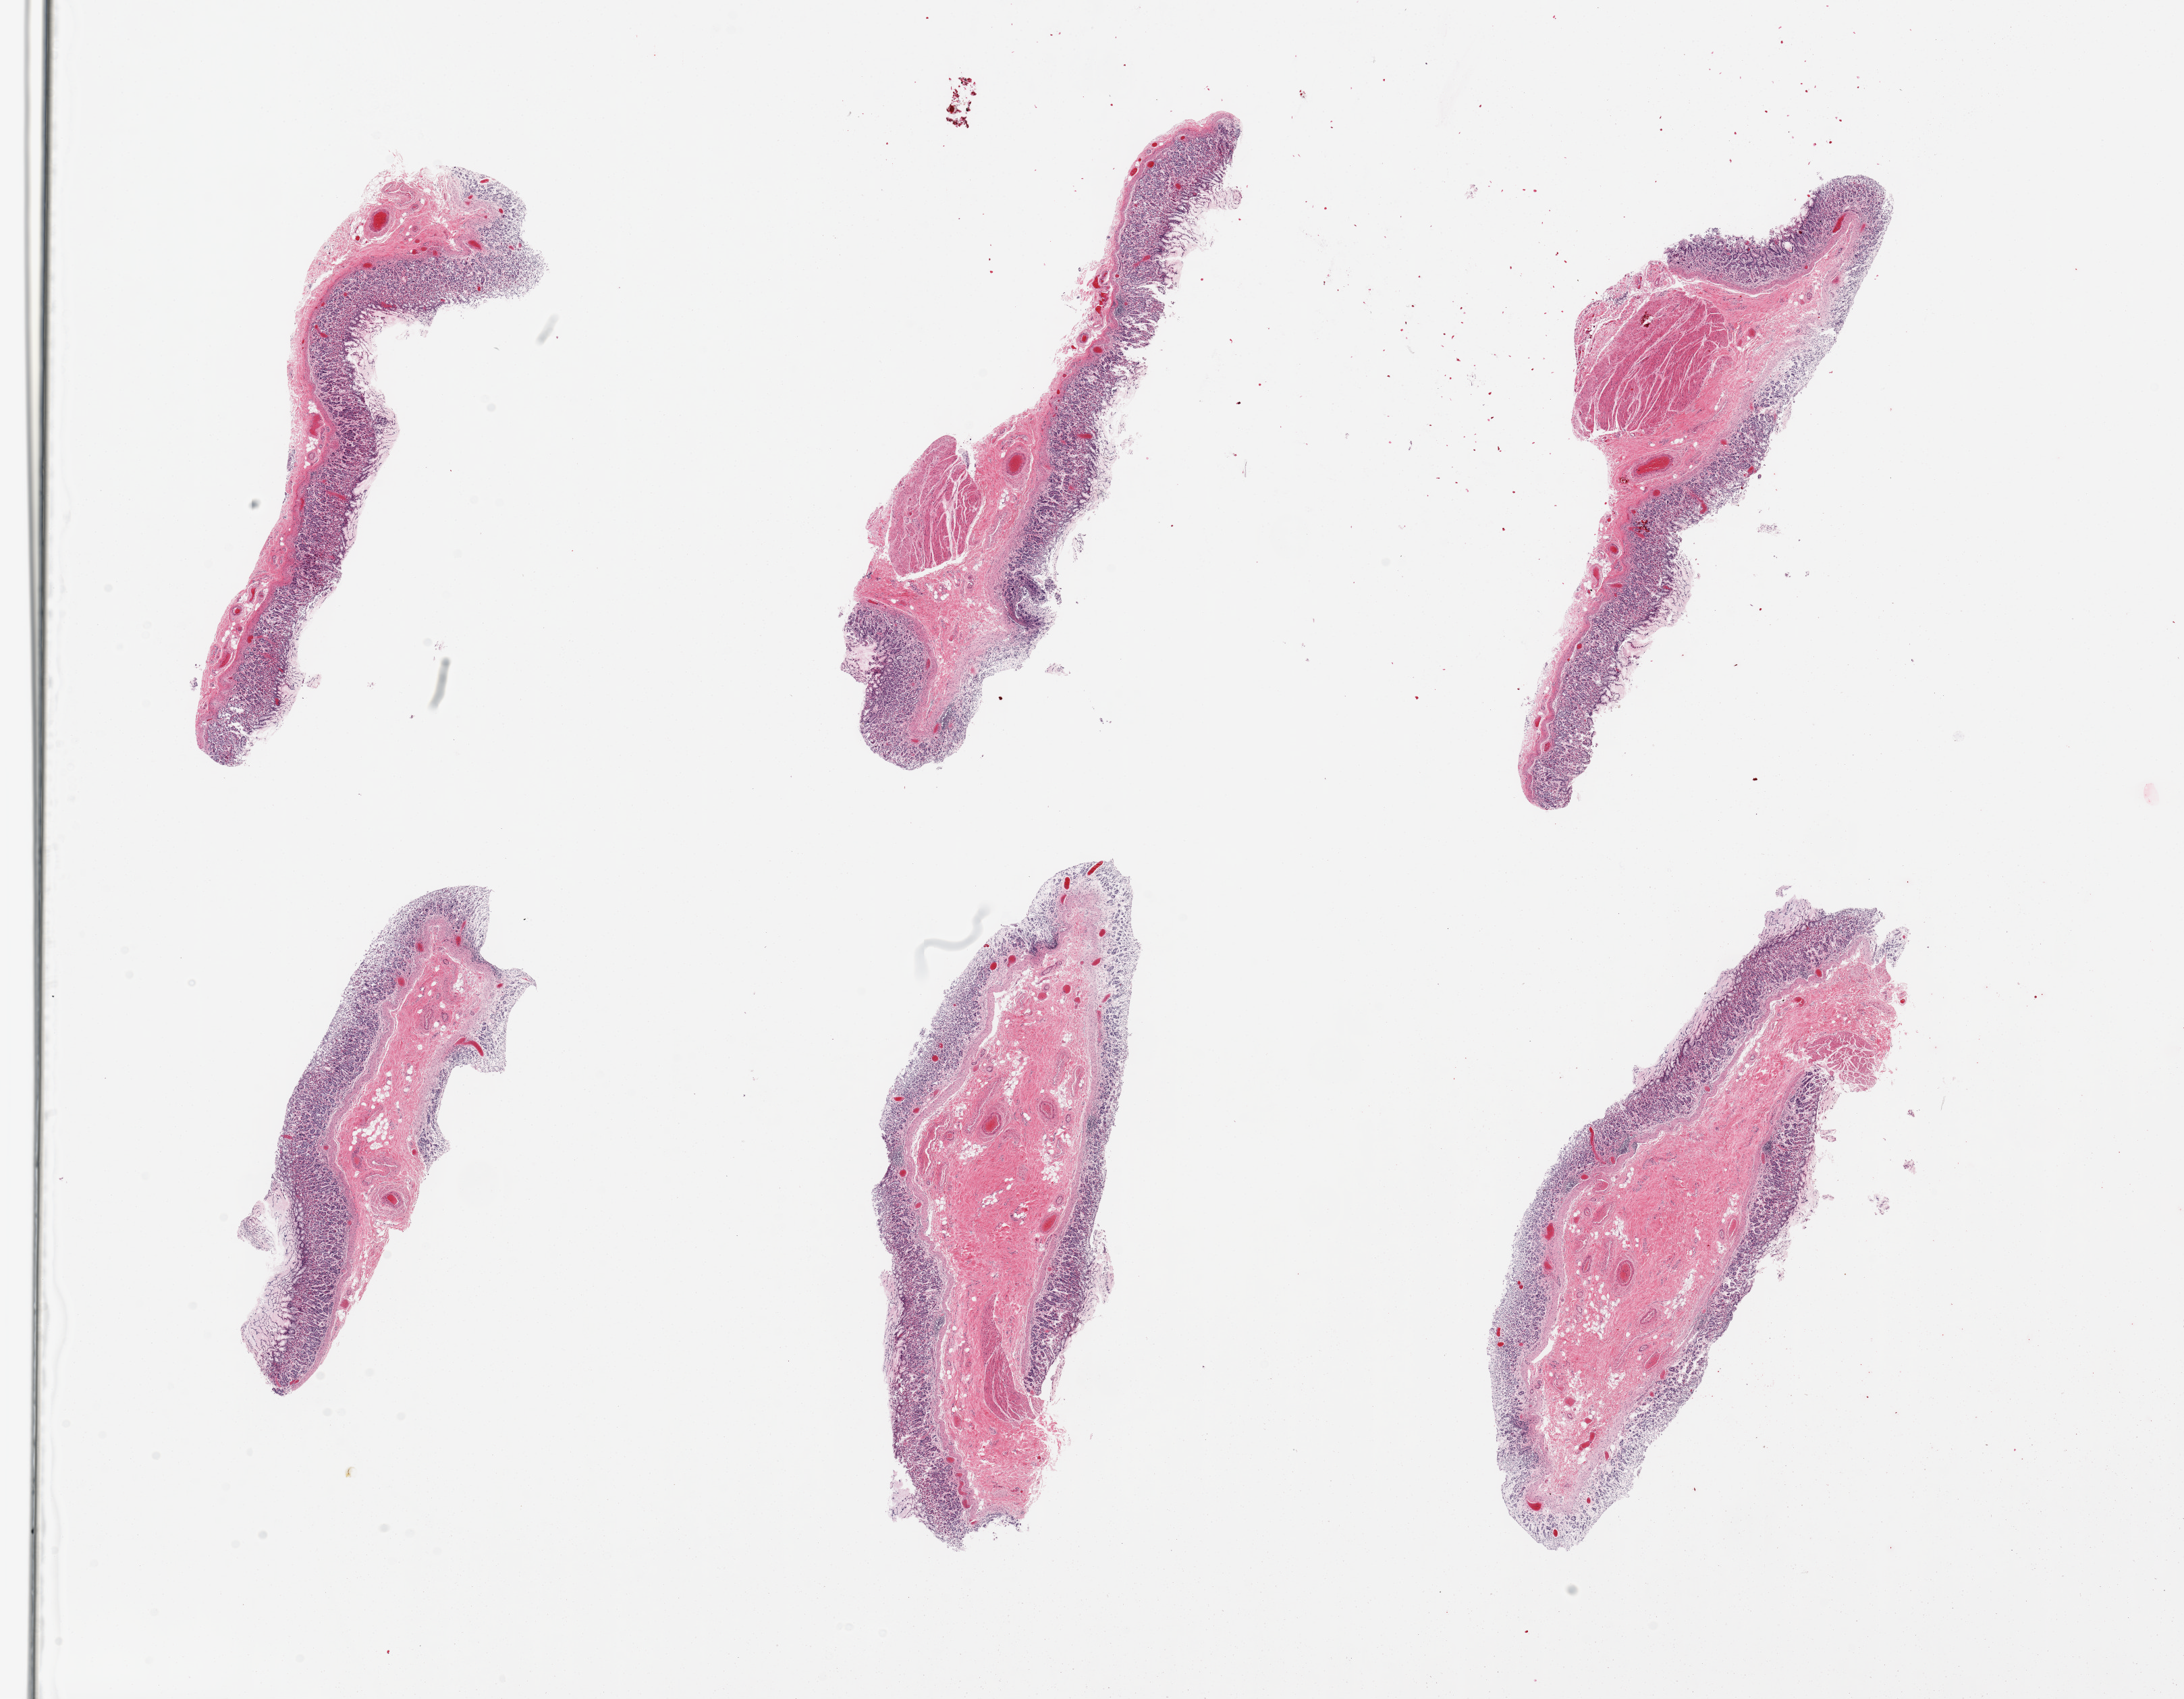
Haematoxylin and eosin whole-slide image, low-resolution overview of the scanned area, about 25.6 x 19.9 mm; PAXgene-fixed, paraffin-embedded tissue; section of stomach (target tissue); tissue donor sample. Female donor.
- reviewer comment on this tissue sample: 6 pieces, mucosa is 50-80% thickness but badly autolyzed, focally a '3', and focally sloughed